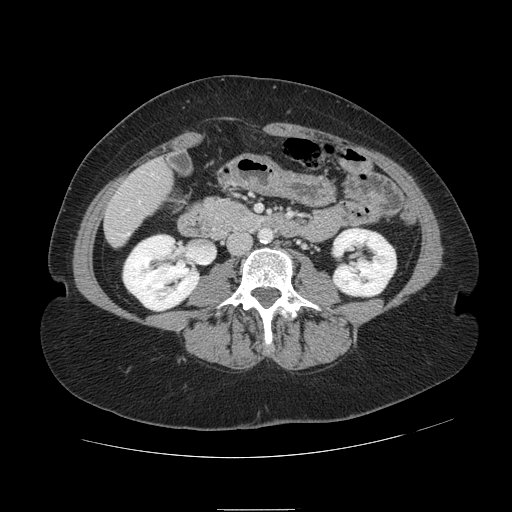
Contrast-enhanced abdominal CT, one axial slice. Slice 16 of 121 in the series (ordered by position). Intravenous contrast given. Soft-tissue window (W 400 / L 40 HU). 2.5 mm slice thickness. 512 × 512 image matrix, field of view 400 × 400 mm. Female patient, age 52 years. Case-level facts recorded for this patient, not image findings: diagnosis: colorectal cancer liver metastases, imaged before liver resection; multiple liver metastases: yes; largest metastasis: 6.3 cm.
Annotated regions visible in this slice (outlined manually by an expert reader):
- hepatic veins: bounding box [x1, y1, x2, y2] px = [122, 174, 153, 237]
- liver: [106, 162, 170, 244]